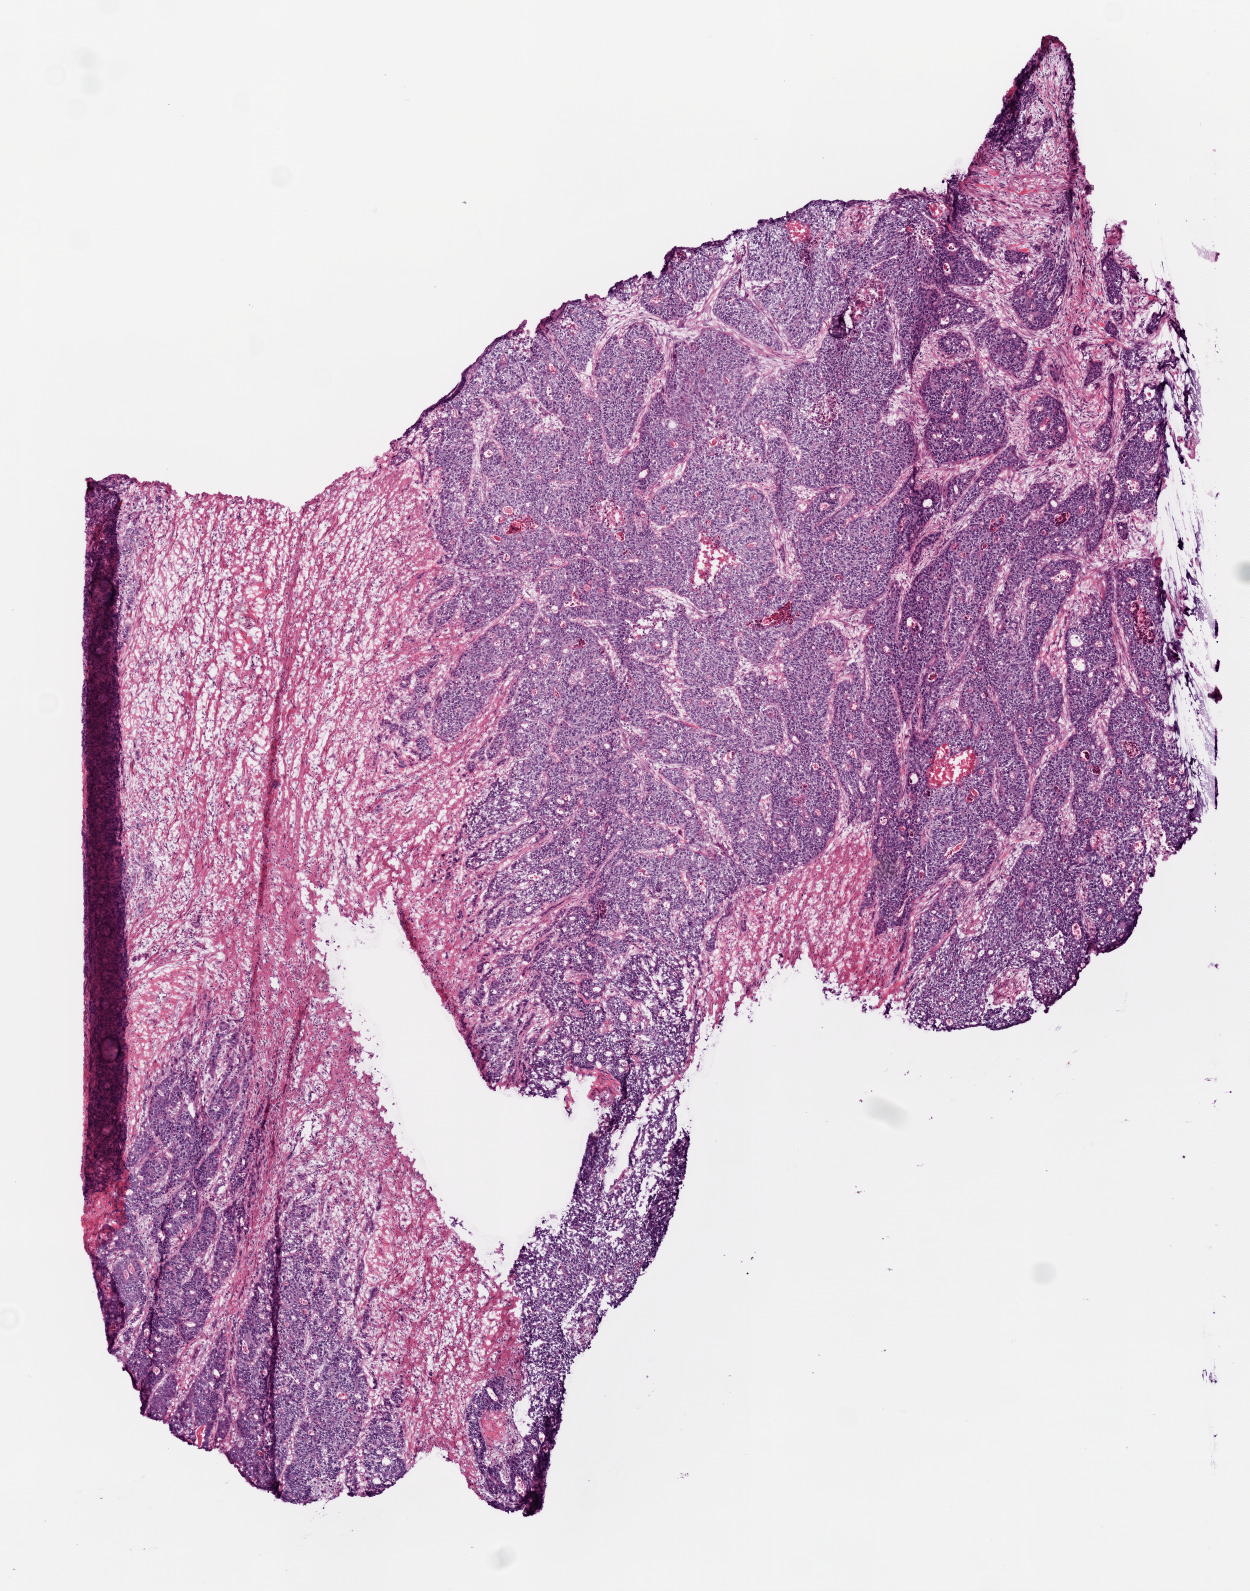
H&E-stained whole-slide image — low-resolution overview of the scanned area, about 5.0 x 6.4 mm (slide scanned at 20x), frozen section, primary tumour sample from the rectum. Female, age 61 years at initial diagnosis. Pathologist review of this section (percent, as recorded): tumour cells 75%, tumour nuclei 85%, normal cells 0%, stromal cells 20%, necrosis 5%.
- AJCC pathologic stage: IIIC (6th edition)
- diagnosis: Adenocarcinoma, NOS (rectosigmoid junction)